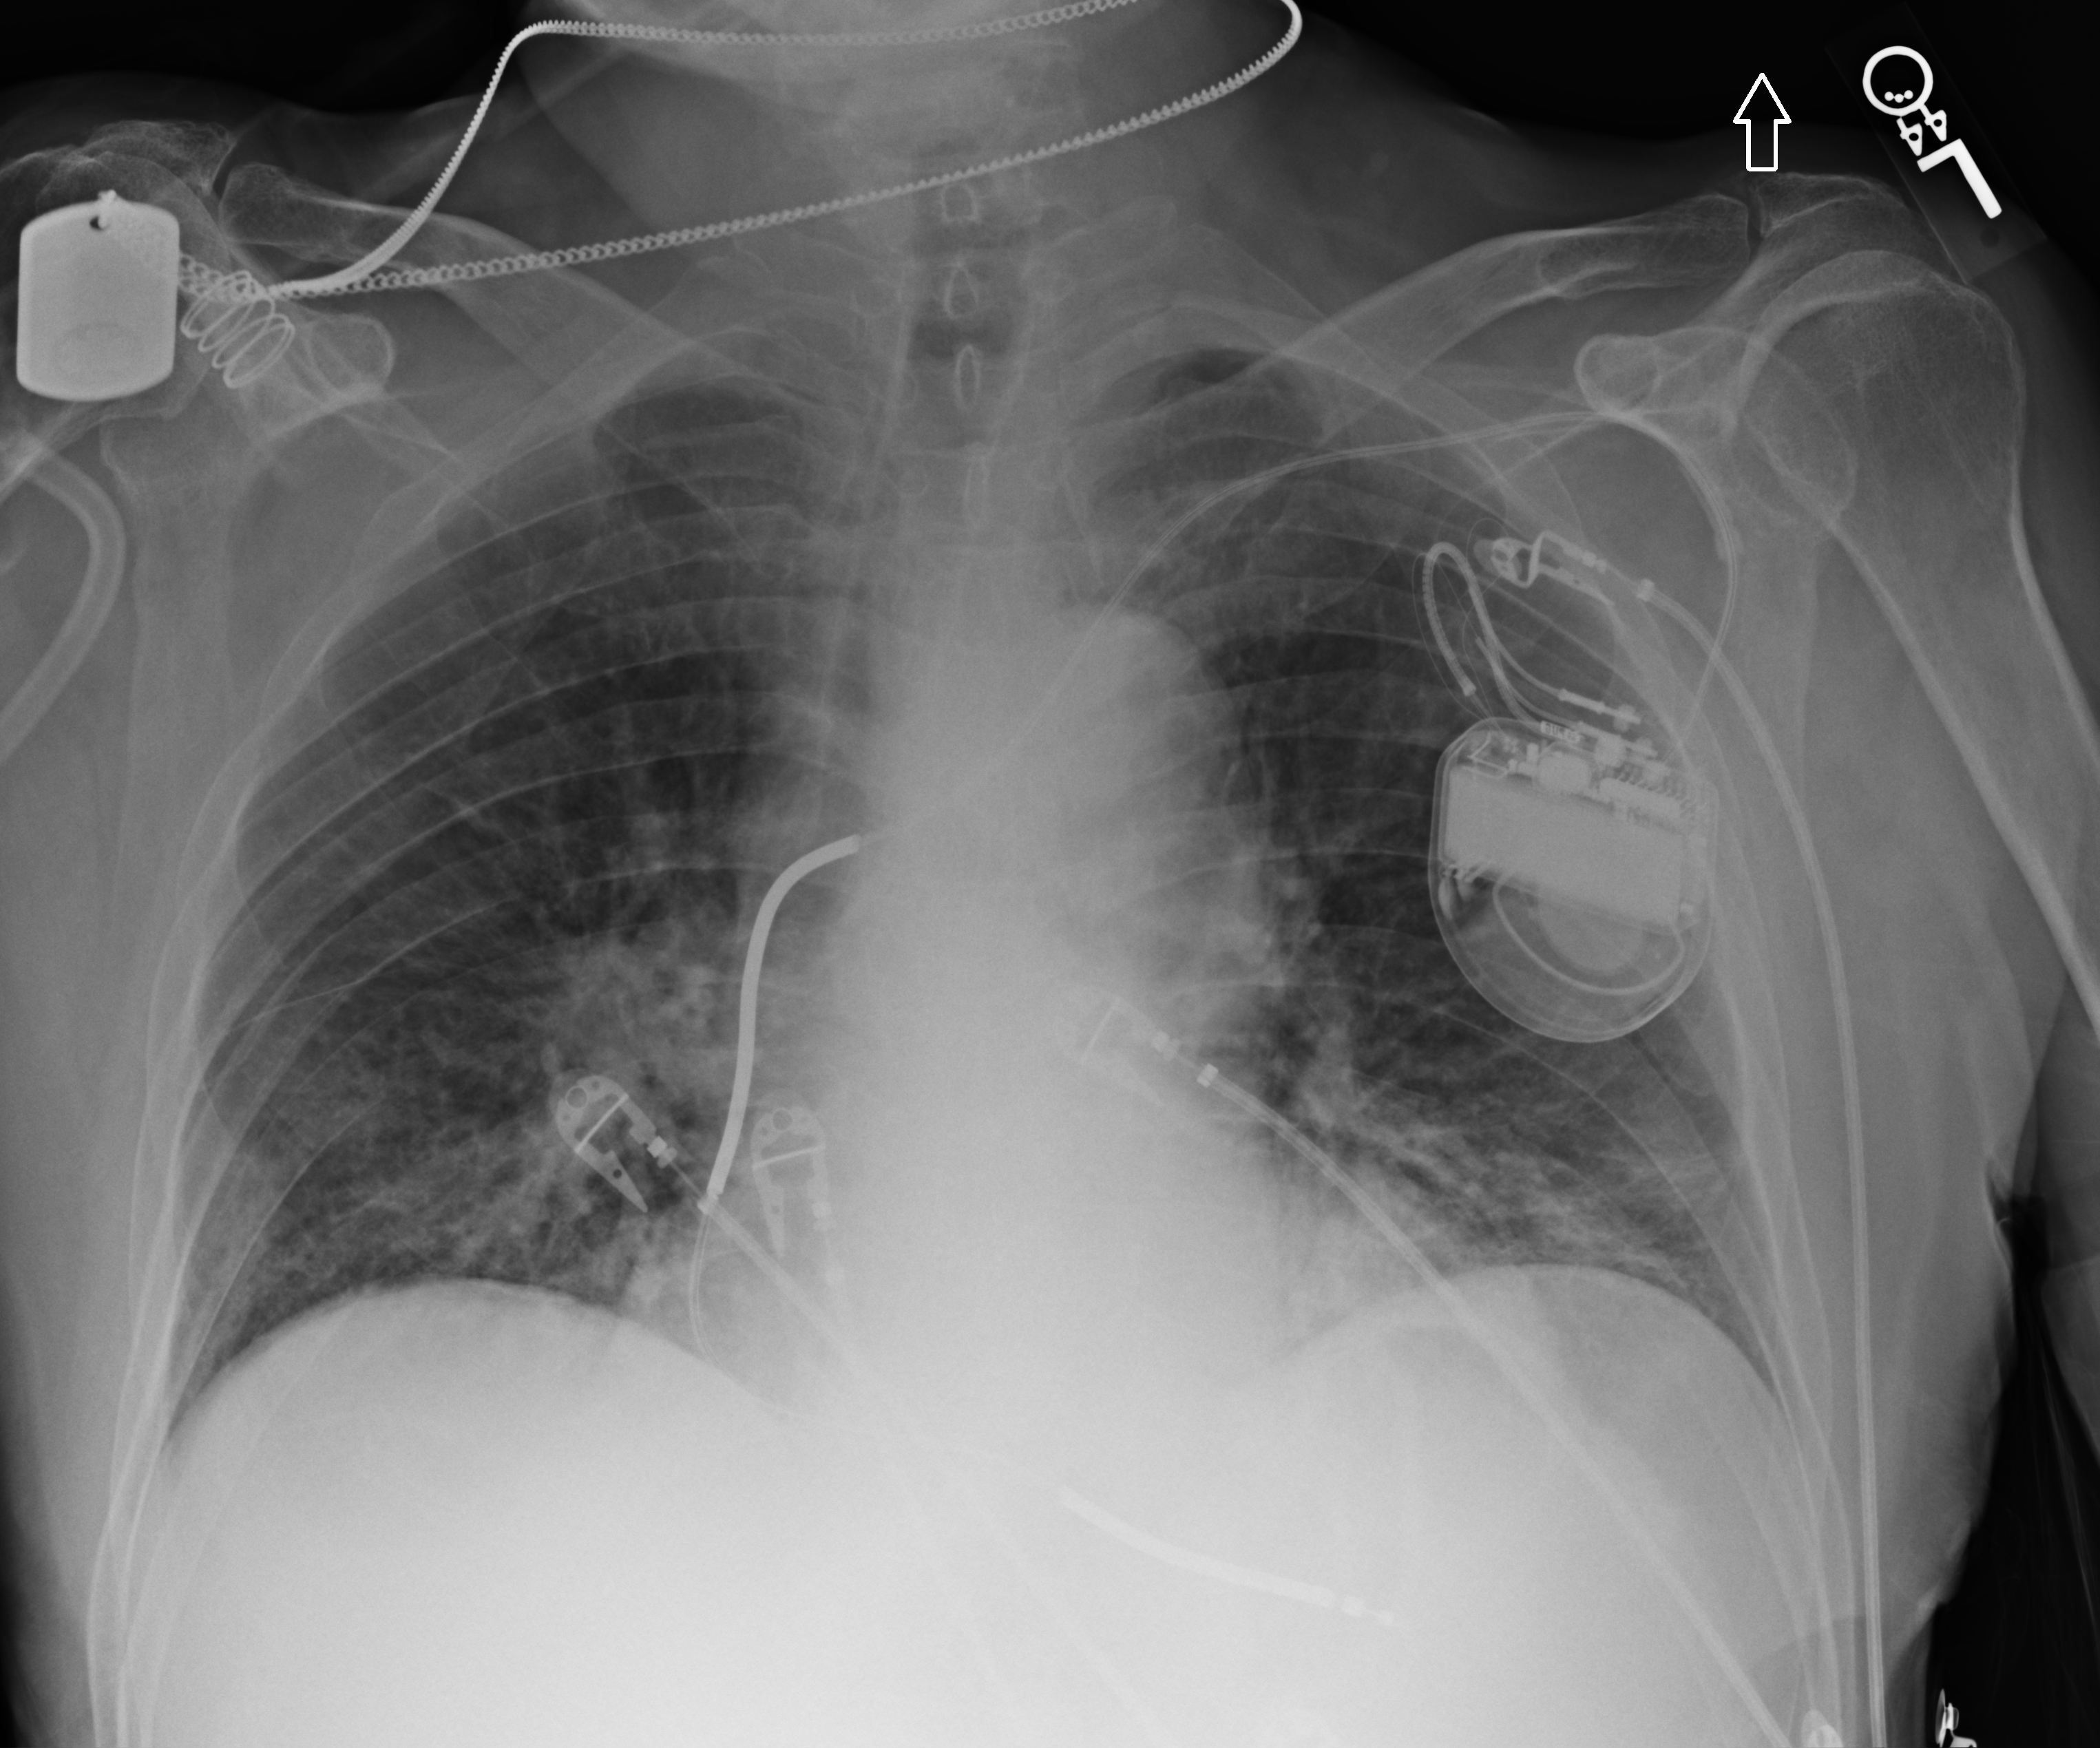
Chest X-ray (portable). Patient hospitalised with COVID-19; male, aged 75–90 years.
Admission-level facts for this patient (not findings on this image; timing relative to this image not recorded): admitted to intensive care during this hospital stay: no.